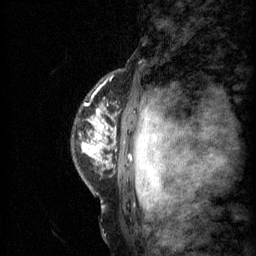
Breast MRI (dynamic contrast-enhanced), one sagittal slice. Slice 50 of 60 in the series (ordered by position). 3 images stored at this slice position (order not interpretable as contrast timing). 1.5 T. TE 4.2 ms, TR 11 ms. 2 mm slice thickness. 256 × 256 image matrix, field of view 200 × 200 mm. Female patient, age 48 years.
Structures marked on this image (semi-automatically segmented with operator editing):
- analysis volume of interest (the breast-tissue region the enhancement analysis was run in; not a lesion): bounding box <81,104,136,147> (left, top, right, bottom; pixels)
- tumour enhancement mask (voxels above the 70 % enhancement threshold inside the analysis volume of interest): <83,124,109,147>